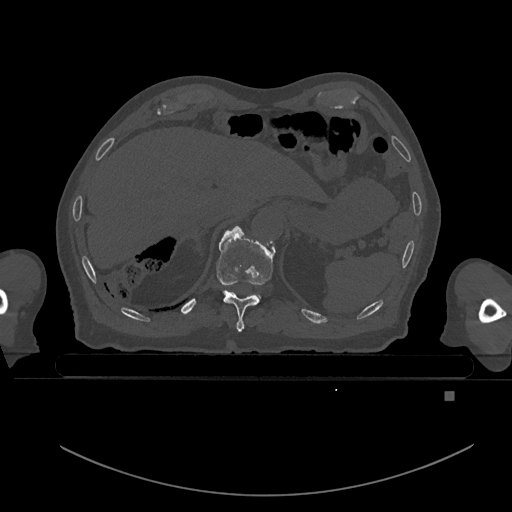
CT including the spine, one axial slice. Slice 79 of 969 in the series (ordered by position). Bone window (W 1800 / L 400 HU). 512 × 512 image matrix, field of view 456 × 456 mm. Male patient, age 82 years. From the clinical record (not read from this slice): primary cancer: prostate; vertebrae with lytic lesions (as recorded): T11, T9, T8, T2.
Outlined on this slice (semi-automatic segmentation, software-assisted and operator-edited):
- T10 vertebra: bounding box (x1, y1, x2, y2) in pixels: (217, 226, 275, 331)